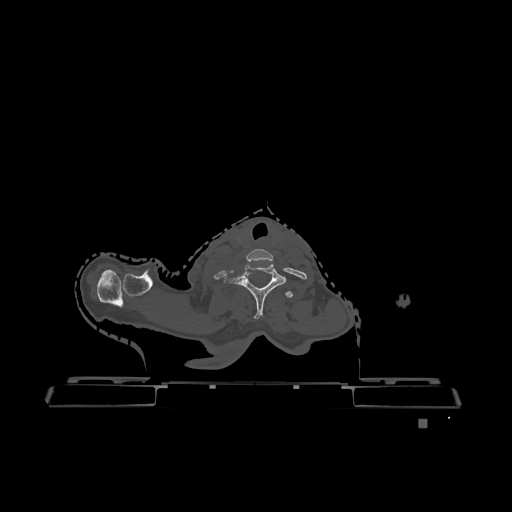
CT including the spine, one axial slice; bone window (W 1800 / L 400 HU); 0.5 mm slice thickness; 512 × 512 image matrix. Patient: female, 74 years. Case-level facts recorded for this patient, not image findings: primary cancer: lung; vertebrae with lytic lesions (as recorded): T1, T4, T5, T6, L4, L5.
Outlined on this slice (semi-automatically segmented with operator editing):
- T1 vertebra: bounding box <285,291,293,298> (left, top, right, bottom; pixels)